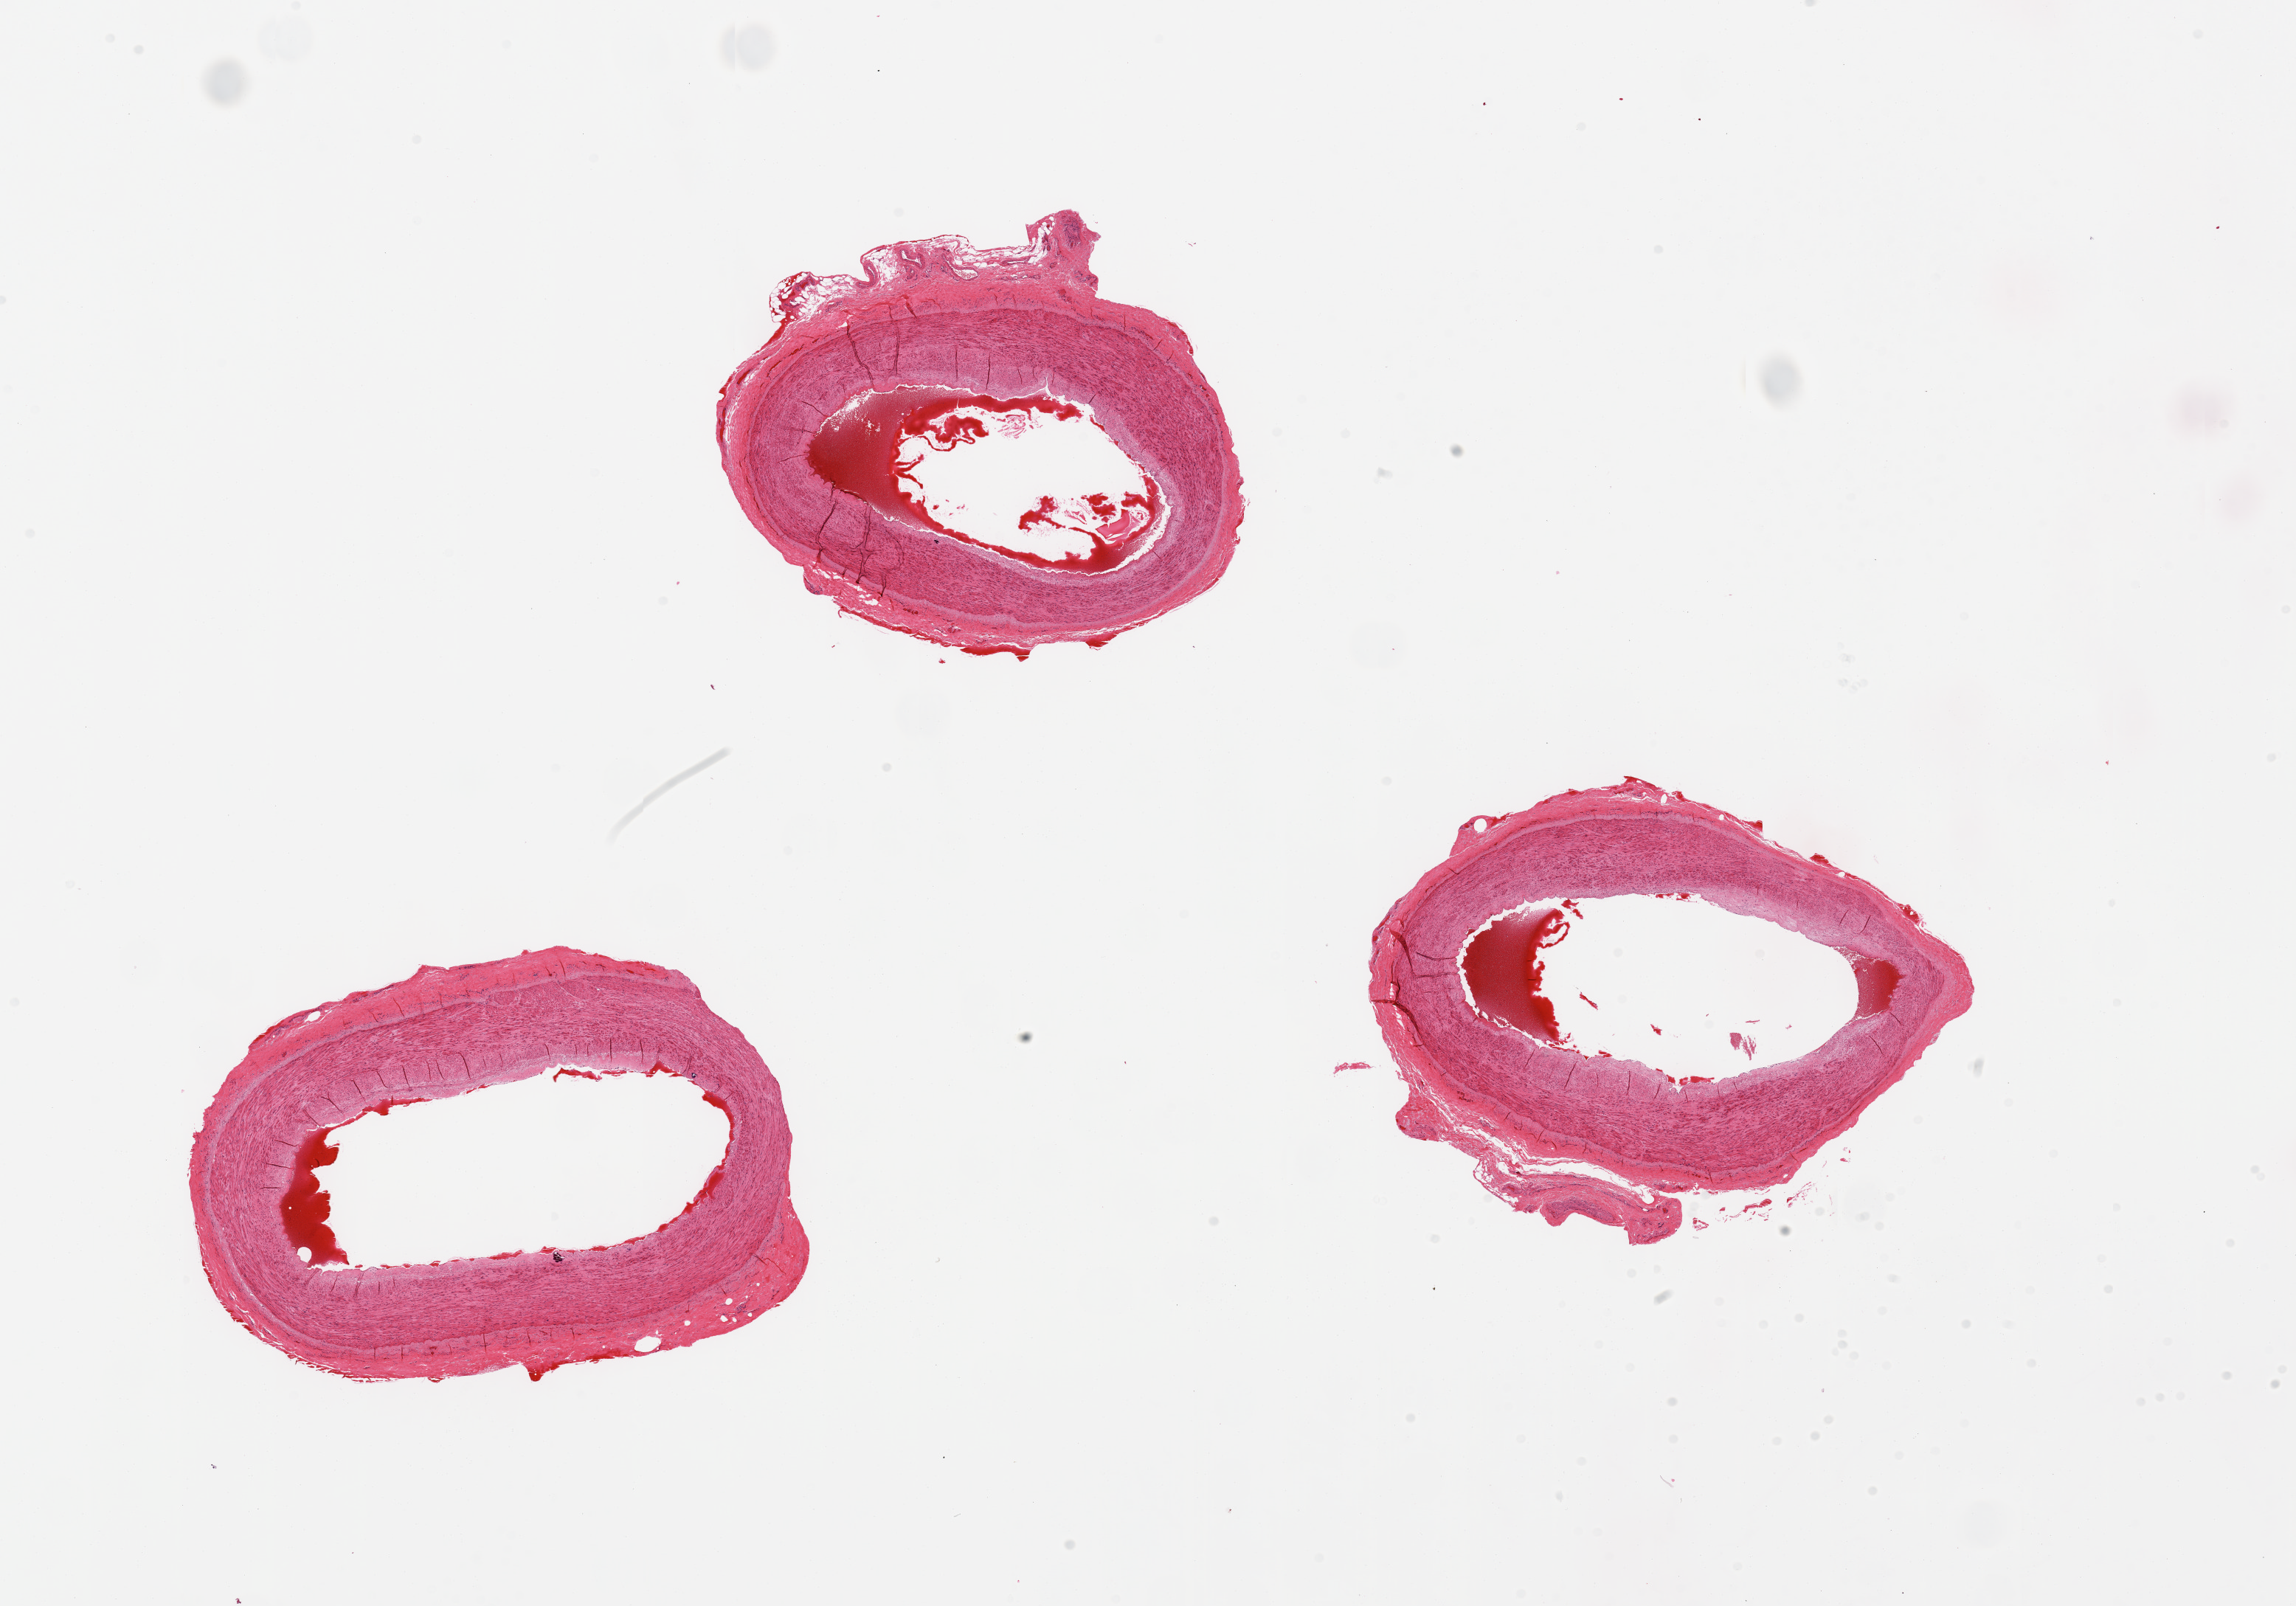
Haematoxylin and eosin whole-slide image, brightfield — low-resolution overview of the scanned area, about 24.6 x 17.2 mm, PAXgene-fixed paraffin-embedded (PFPE) section, target tissue: tibial artery, donor tissue sample. Male donor.
- reviewer comment on this tissue sample: 3 pieces, minimal adherent fat, good specimen, mild atherosis